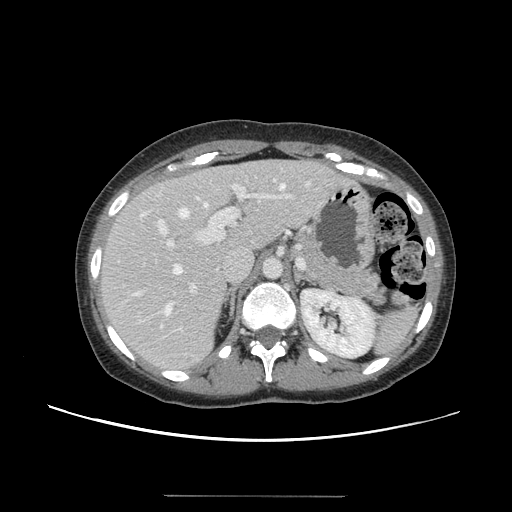
Contrast-enhanced abdominal CT, one axial slice. Slice 92 of 144 in the series (ordered by position). Intravenous contrast given. Soft-tissue window (W 400 / L 40 HU). 512 × 512 image matrix, field of view 380 × 380 mm. Female patient, age 53 years. Case-level facts recorded for this patient, not image findings: diagnosis: colorectal cancer liver metastases, imaged before liver resection; multiple liver metastases: yes; largest metastasis: 1.1 cm; chemotherapy before resection: no.
Outlined on this slice (outlined manually by an expert reader):
- hepatic veins: bounding box [x1, y1, x2, y2] px = [135, 182, 309, 314]
- liver: [99, 160, 343, 371]
- planned liver remnant (the part of the liver to remain after resection): [99, 160, 311, 298]
- portal vein (with intrahepatic branches): [157, 178, 293, 293]